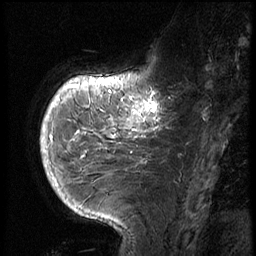
Breast MRI (dynamic contrast-enhanced), one sagittal slice; position 18 of 72 along the scan axis; 3 images stored at this slice position (order not interpretable as contrast timing); 1.5 T; TE 4.2 ms, TR 8.9 ms; 256 × 256 image matrix, field of view 200 × 200 mm. Female patient, age 56 years. From the clinical record (not read from this slice): setting: breast cancer imaged before/during neoadjuvant chemotherapy.
Structures marked on this image (semi-automatic segmentation, software-assisted and operator-edited):
- analysis volume of interest (the breast-tissue region the enhancement analysis was run in; not a lesion): bounding box (x1, y1, x2, y2) in pixels: (114, 76, 177, 138)
- tumour enhancement mask (voxels above the 140 % enhancement threshold inside the analysis volume of interest): (131, 92, 159, 138)